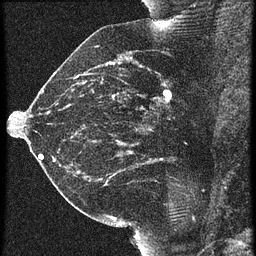
Breast MRI (dynamic contrast-enhanced), one sagittal slice; slice 26 of 60 in the series (ordered by position); 3 images stored at this slice position (order not interpretable as contrast timing); 1.5 T; TE 4.2 ms, TR 21.3 ms; 256 × 256 image matrix. Patient: female, 42 years. Case-level facts recorded for this patient, not image findings: setting: breast cancer imaged before/during neoadjuvant chemotherapy; receptor status: HER2-positive.
Structures marked on this image (semi-automatically segmented with operator editing):
- analysis volume of interest (the breast-tissue region the enhancement analysis was run in; not a lesion): bounding box <122,82,195,147> (left, top, right, bottom; pixels)
- tumour enhancement mask (voxels above the 90 % enhancement threshold inside the analysis volume of interest): <122,84,171,145>